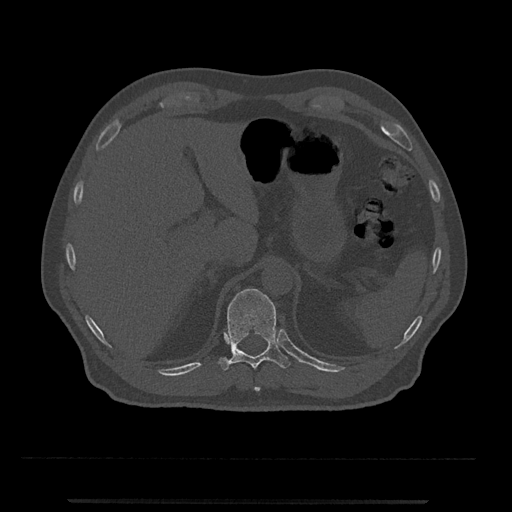
CT including the spine, one axial slice; slice 467 of 797 in the series (ordered by position); reconstruction kernel Br40s/3; 120 kVp; bone window (W 1800 / L 400 HU); 0.5 mm slice thickness; 512 × 512 image matrix, field of view 419 × 419 mm. Patient: male, 63 years. Case-level facts recorded for this patient, not image findings: primary cancer: prostate.
Outlined on this slice (semi-automatic segmentation, software-assisted and operator-edited):
- T10 vertebra: bounding box [x1, y1, x2, y2] px = [254, 387, 260, 392]
- T11 vertebra: [218, 288, 291, 371]